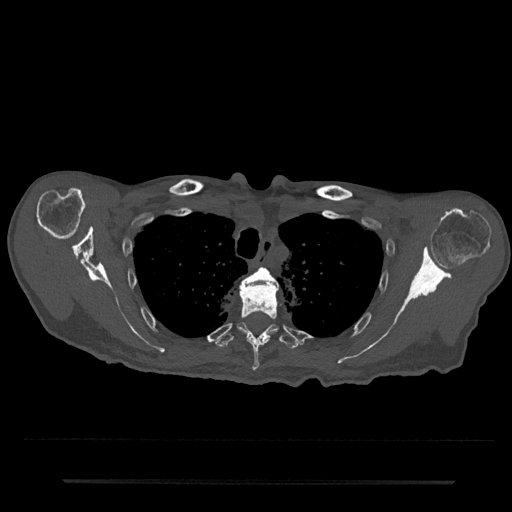
CT including the spine, one axial slice. Position 610 of 797 along the scan axis. 120 kVp. Bone window (W 1800 / L 400 HU). 0.5 mm slice thickness. 512 × 512 image matrix, field of view 427 × 427 mm. Patient: male, 74 years. Case-level facts recorded for this patient, not image findings: primary cancer: prostate.
Outlined on this slice (semi-automatically segmented with operator editing):
- T3 vertebra: bounding box (x1, y1, x2, y2) in pixels: (241, 267, 279, 290)
- T4 vertebra: (239, 282, 278, 371)
- T5 vertebra: (214, 323, 301, 350)